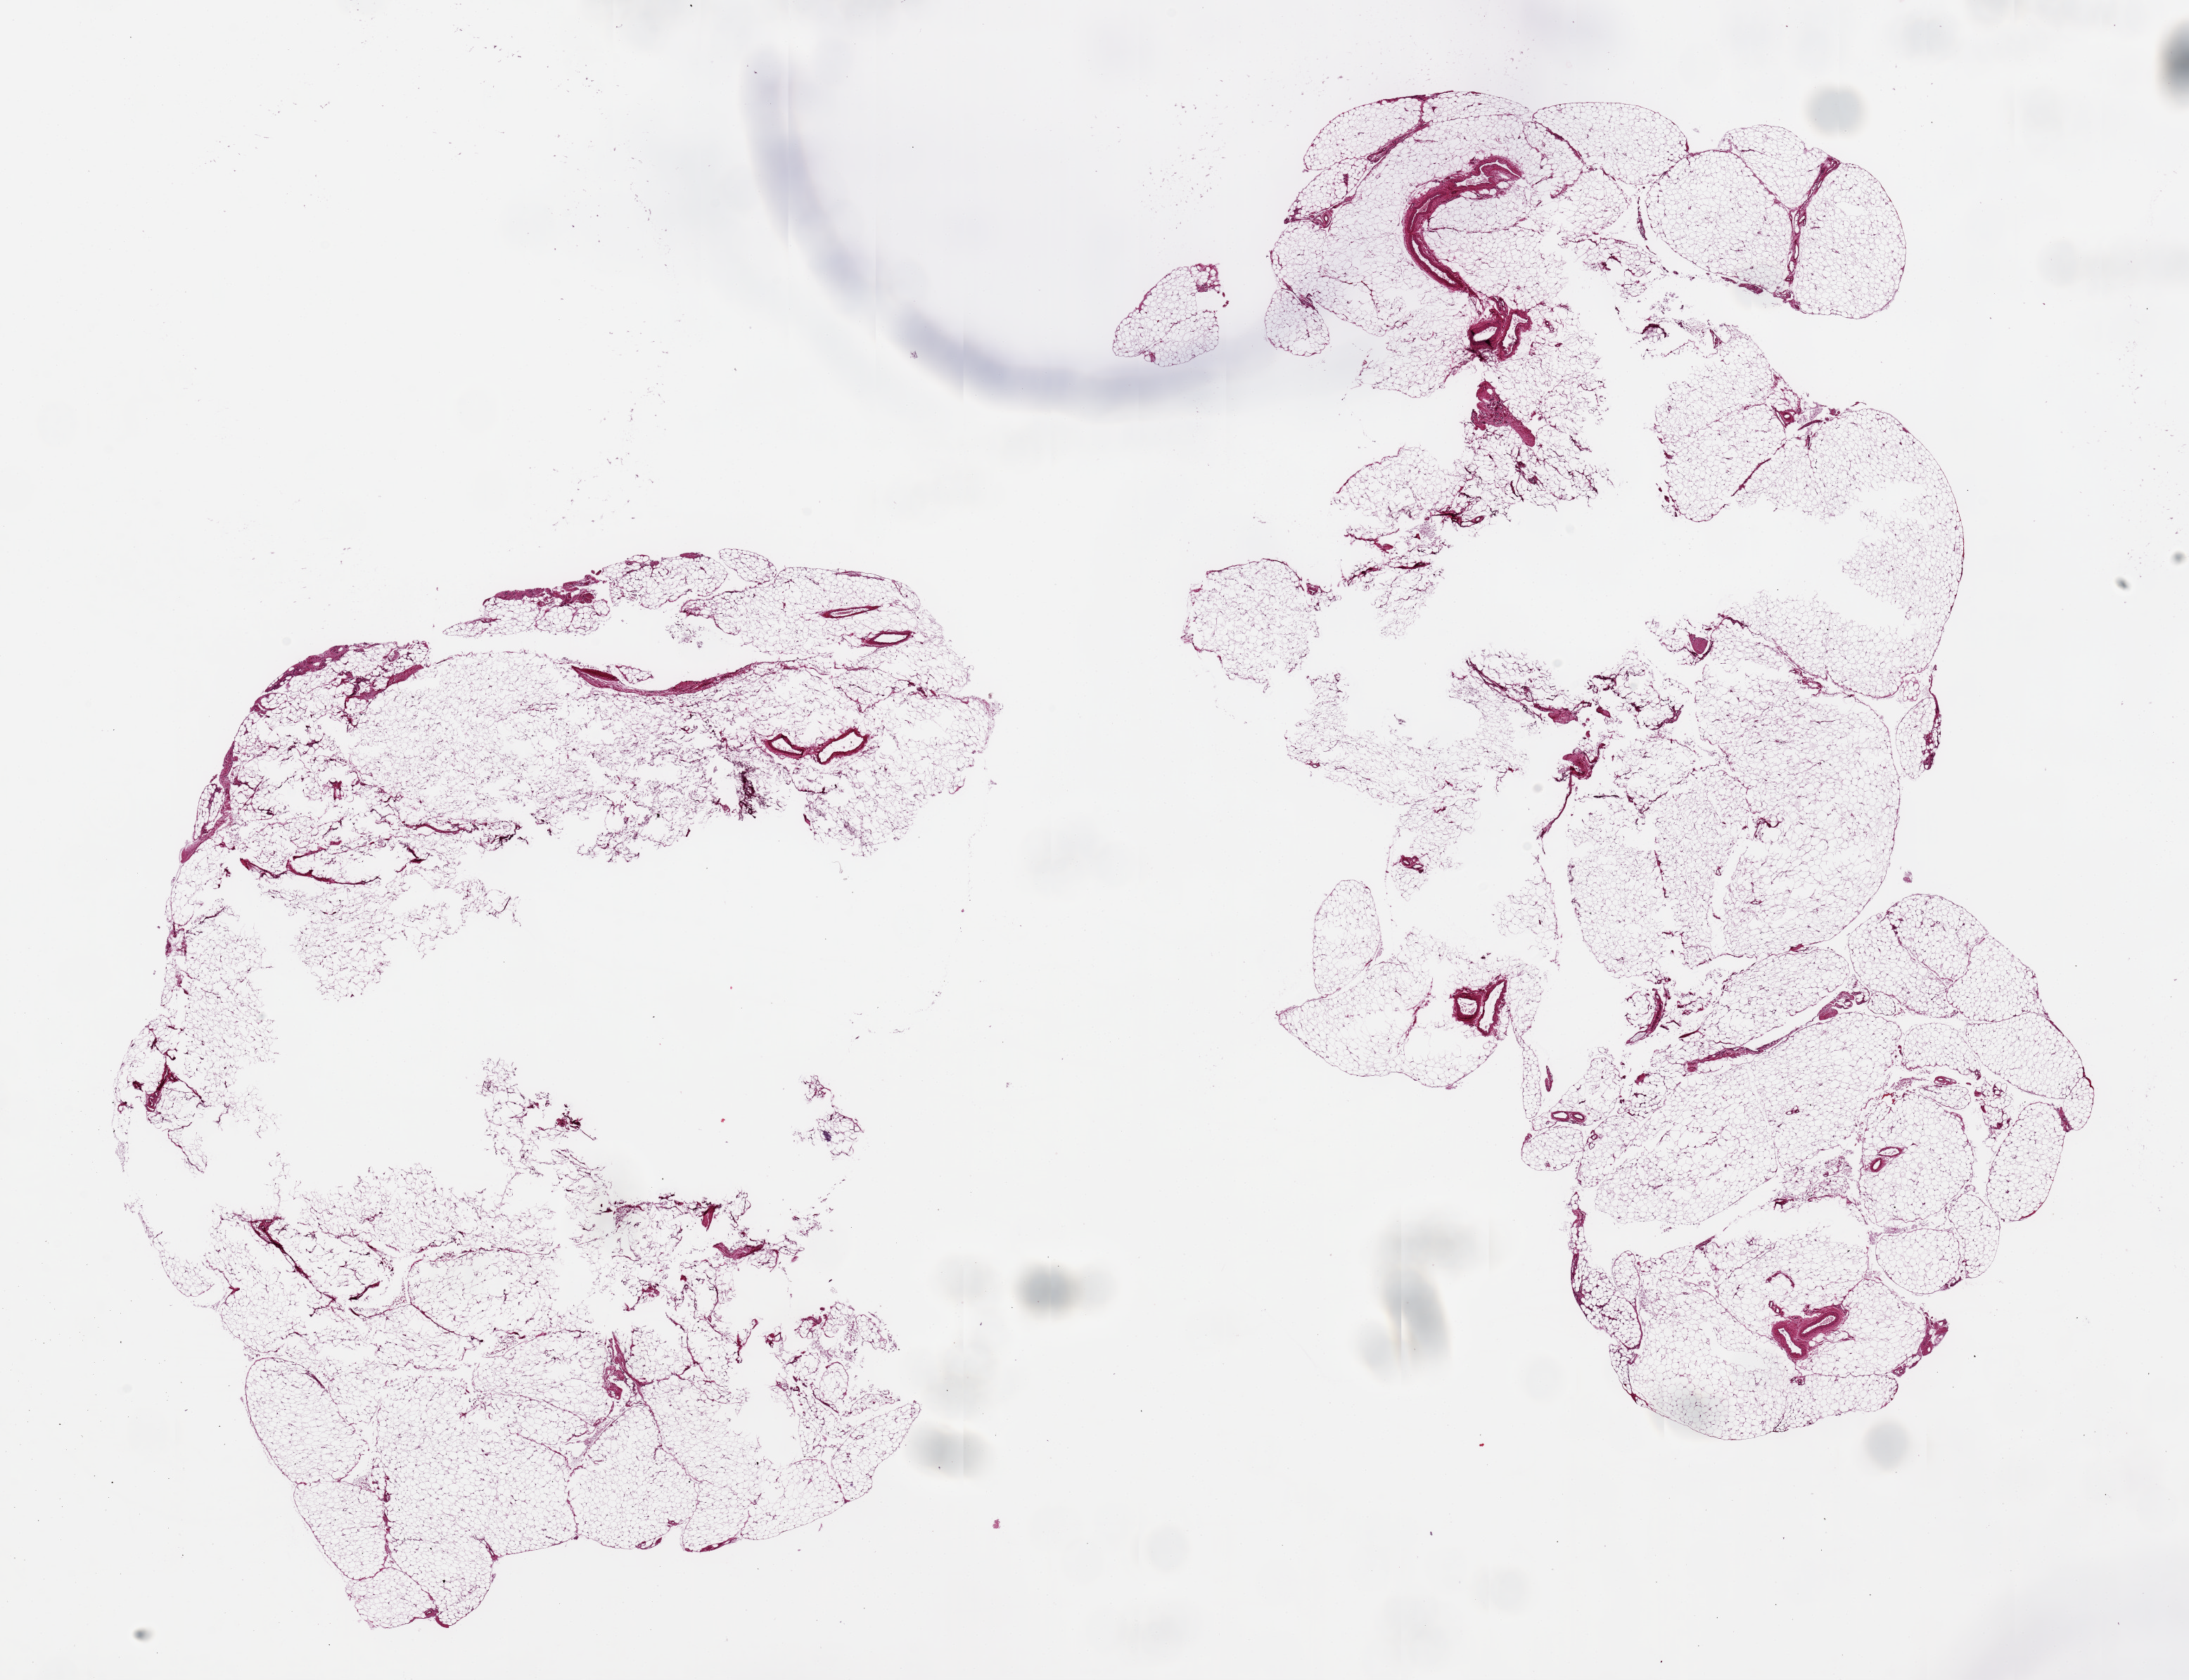
Haematoxylin and eosin whole-slide image, brightfield — low-resolution overview of the scanned area, about 24.6 x 18.9 mm (slide scanned at 20x); PAXgene-fixed, paraffin-embedded tissue; sampled site (target tissue): pancreas; donor tissue sample. Donor sex: female.
Reviewer comment on this tissue sample: 2 pieces of poorly fixed adipose tissue ~12x9 & 15x8mm; NO PANCREAS.